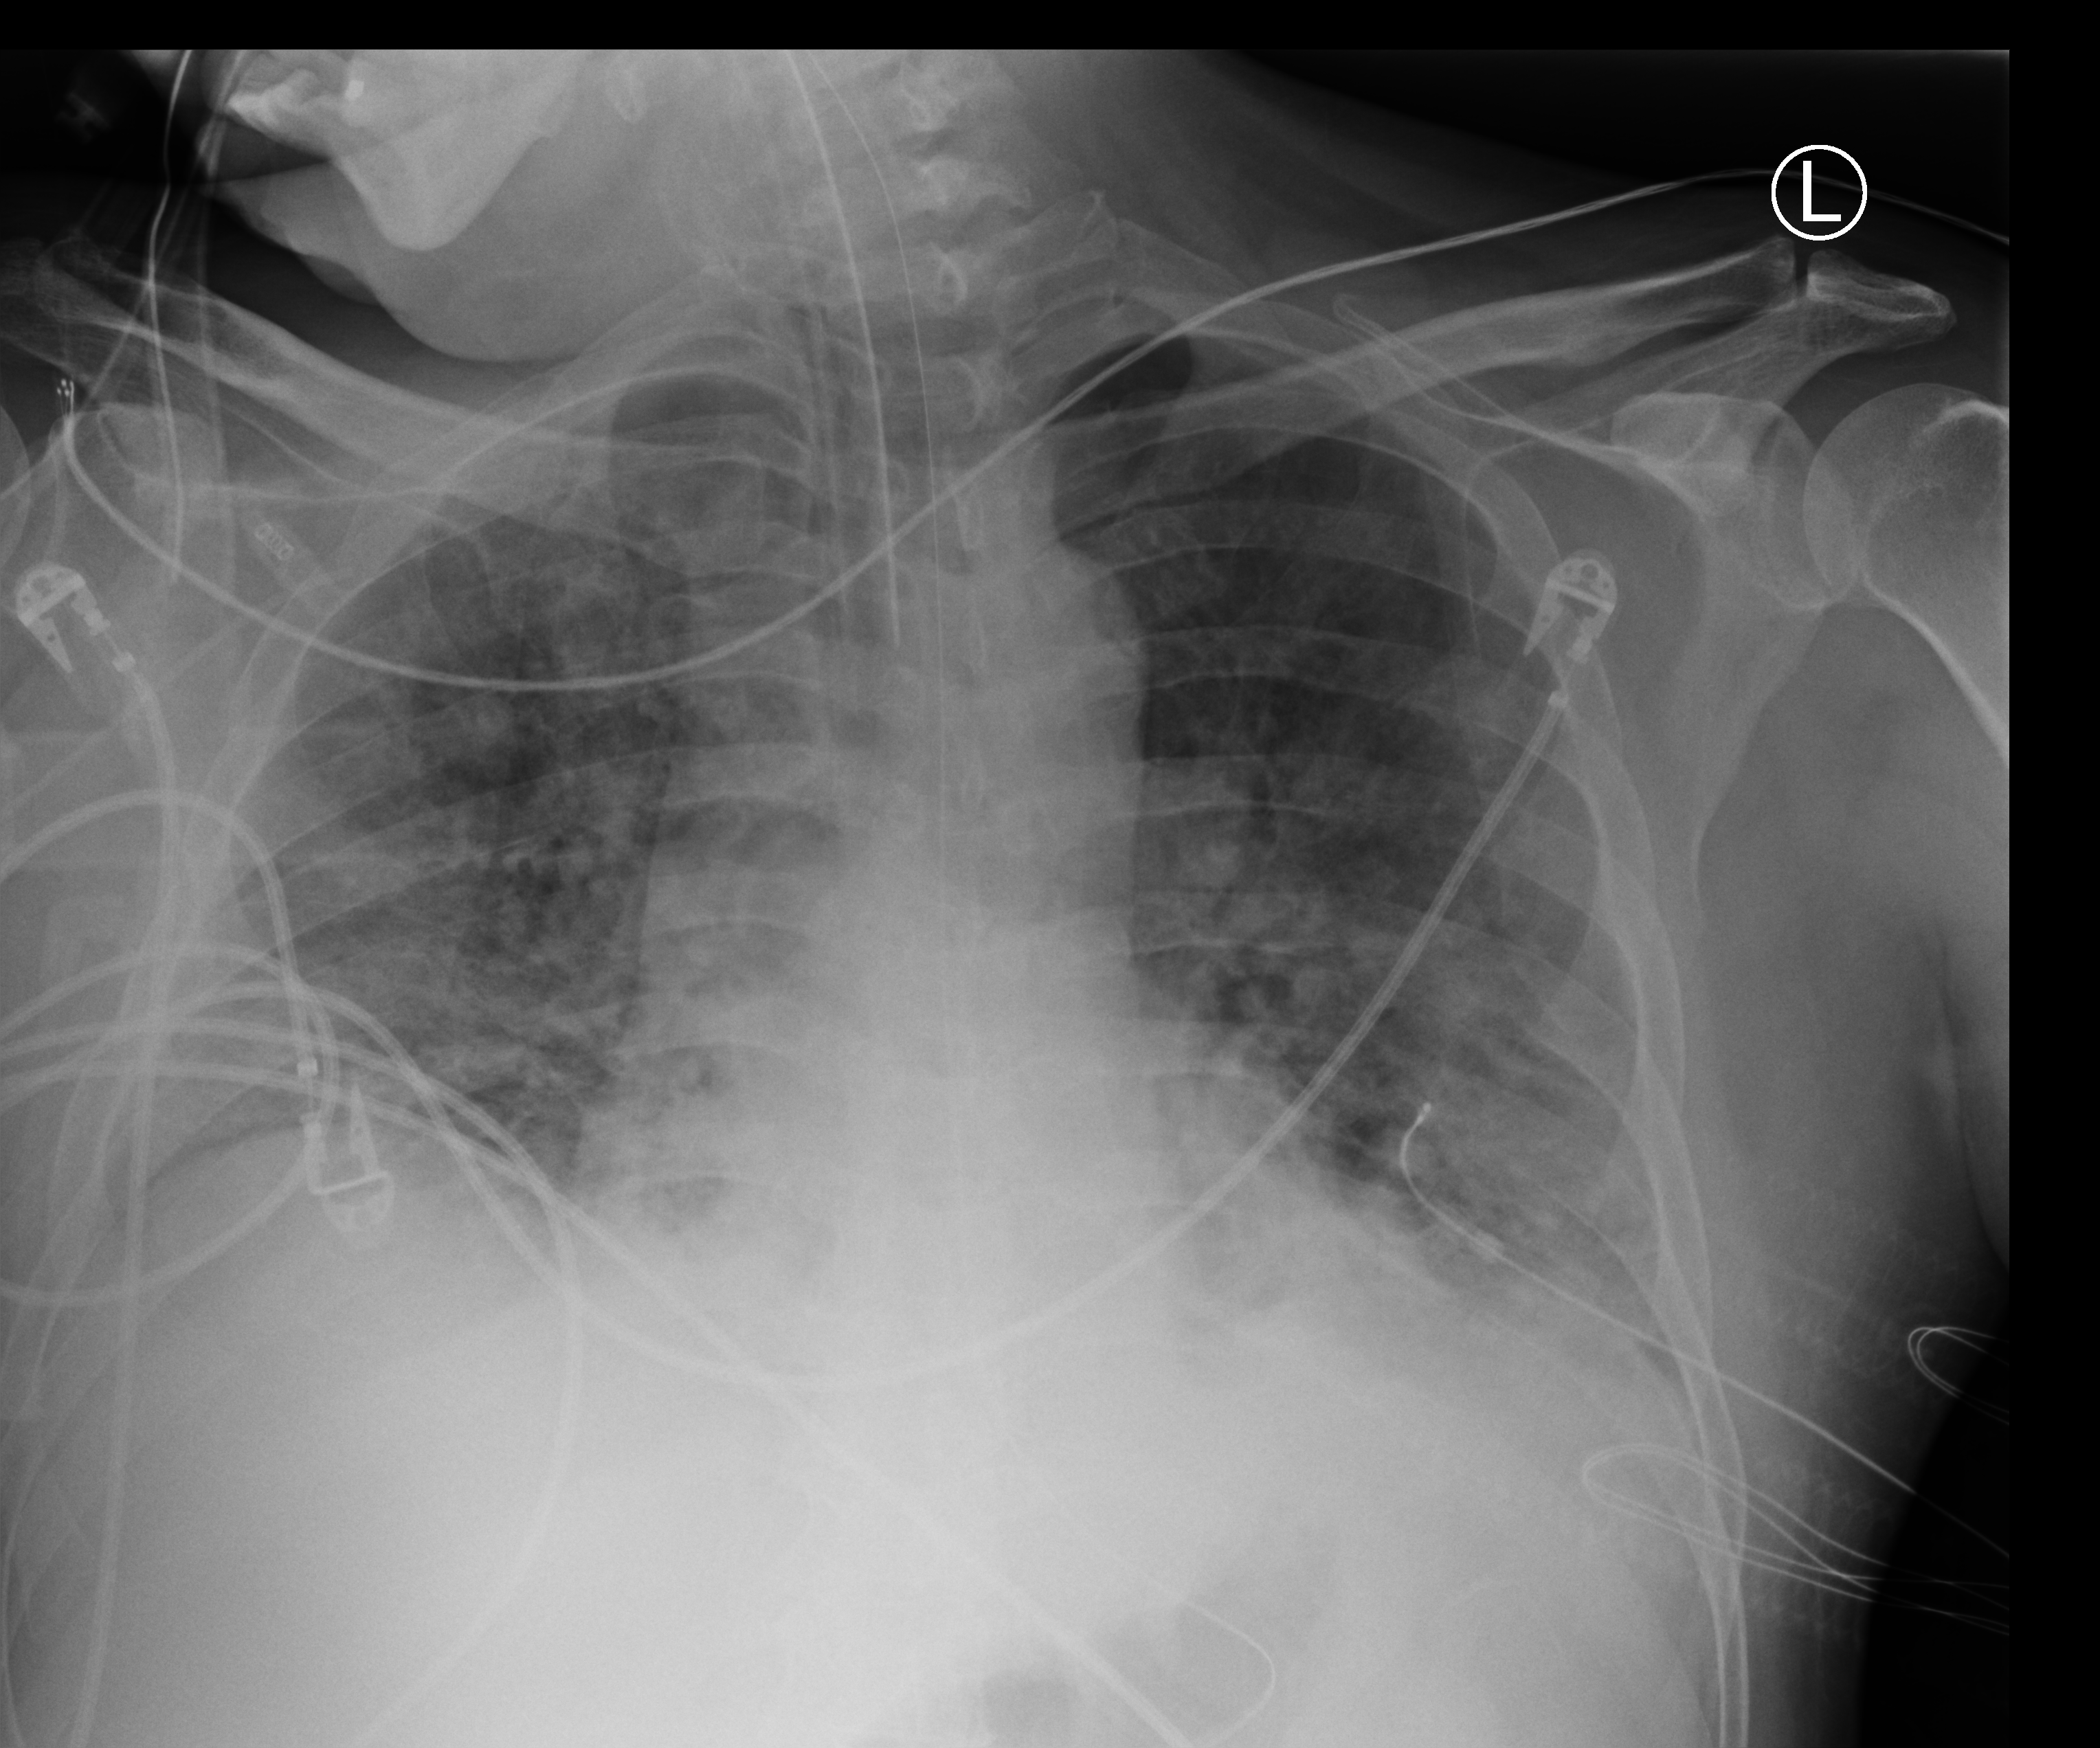
Bedside chest radiograph (computed radiography), anteroposterior (AP) projection. Patient hospitalised with COVID-19; male, aged 18–59 years.
Admission-level facts for this patient (not findings on this image; timing relative to this image not recorded): mechanically ventilated during this hospital stay: yes; hypertension (admission record): yes; admitted to intensive care during this hospital stay: yes.